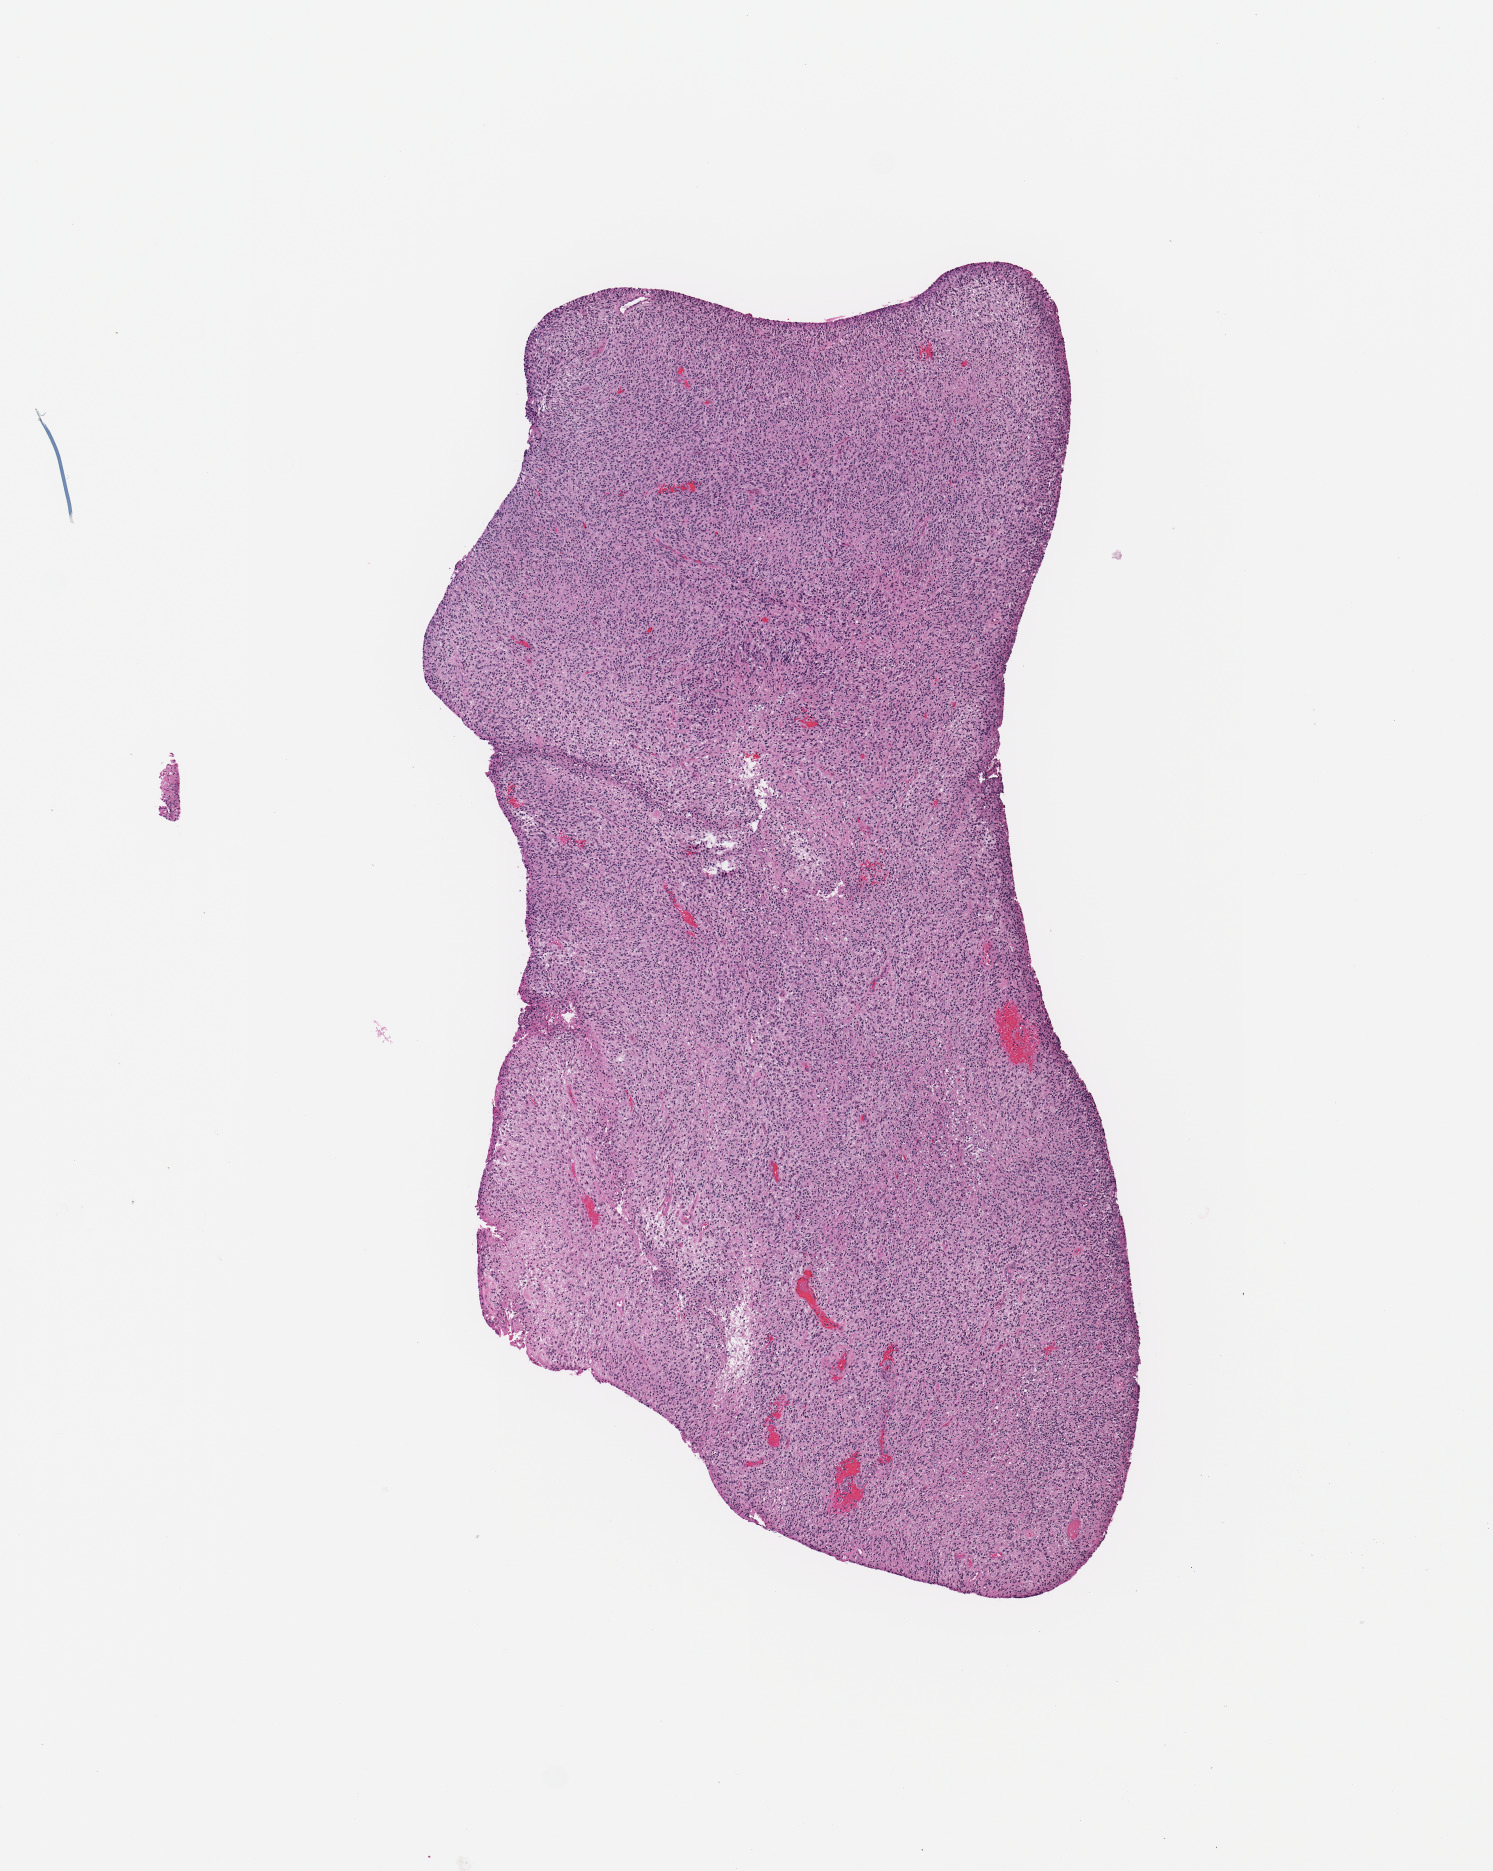
Digitized H&E-stained tissue section (whole slide) — whole scanned area (about 5.9 x 7.4 mm, from a 20x scan) shown as a low-resolution overview. Tumour tissue sample, sampled site: brain. Male, 57 y/o. Pathologist review of this section (percent, as recorded): tumour nuclei 85%, necrosis 5%.
* diagnosis: Glioblastoma